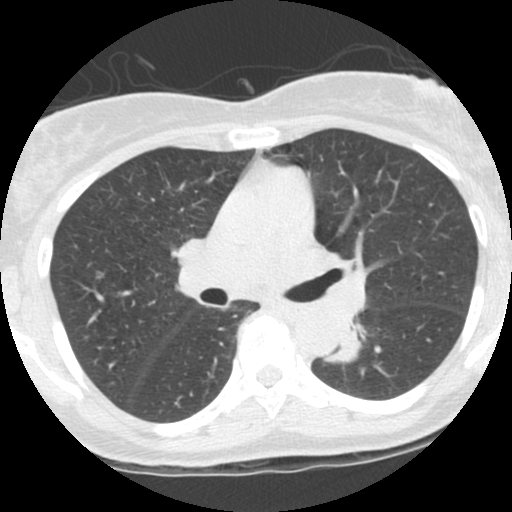
Low-dose screening chest CT, one axial slice; position 65 of 115 along the scan axis; 120 kVp; lung window (W 1500 / L -600 HU); 2.5 mm slice thickness; 512 × 512 image matrix, field of view 290 × 290 mm.
Structures marked on this image (expert manual segmentation):
- lesion 1 (tumor, lower lobe of left lung): bounding box (x1, y1, x2, y2) in pixels: (325, 332, 360, 362)